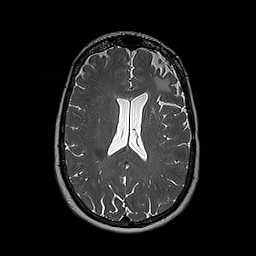
Brain MRI from a brain-tumour surgery series, one axial slice. Slice 111 of 192 in the series (ordered by position). 256 × 256 image matrix, field of view 250 × 250 mm. Case-level facts recorded for this patient, not image findings: histopathology: Oligodendroglioma; WHO grade: 2; IDH mutation: yes.
Annotated regions visible in this slice (manually delineated by an expert):
- tumour: bounding box (x1, y1, x2, y2) in pixels: (152, 76, 161, 113)